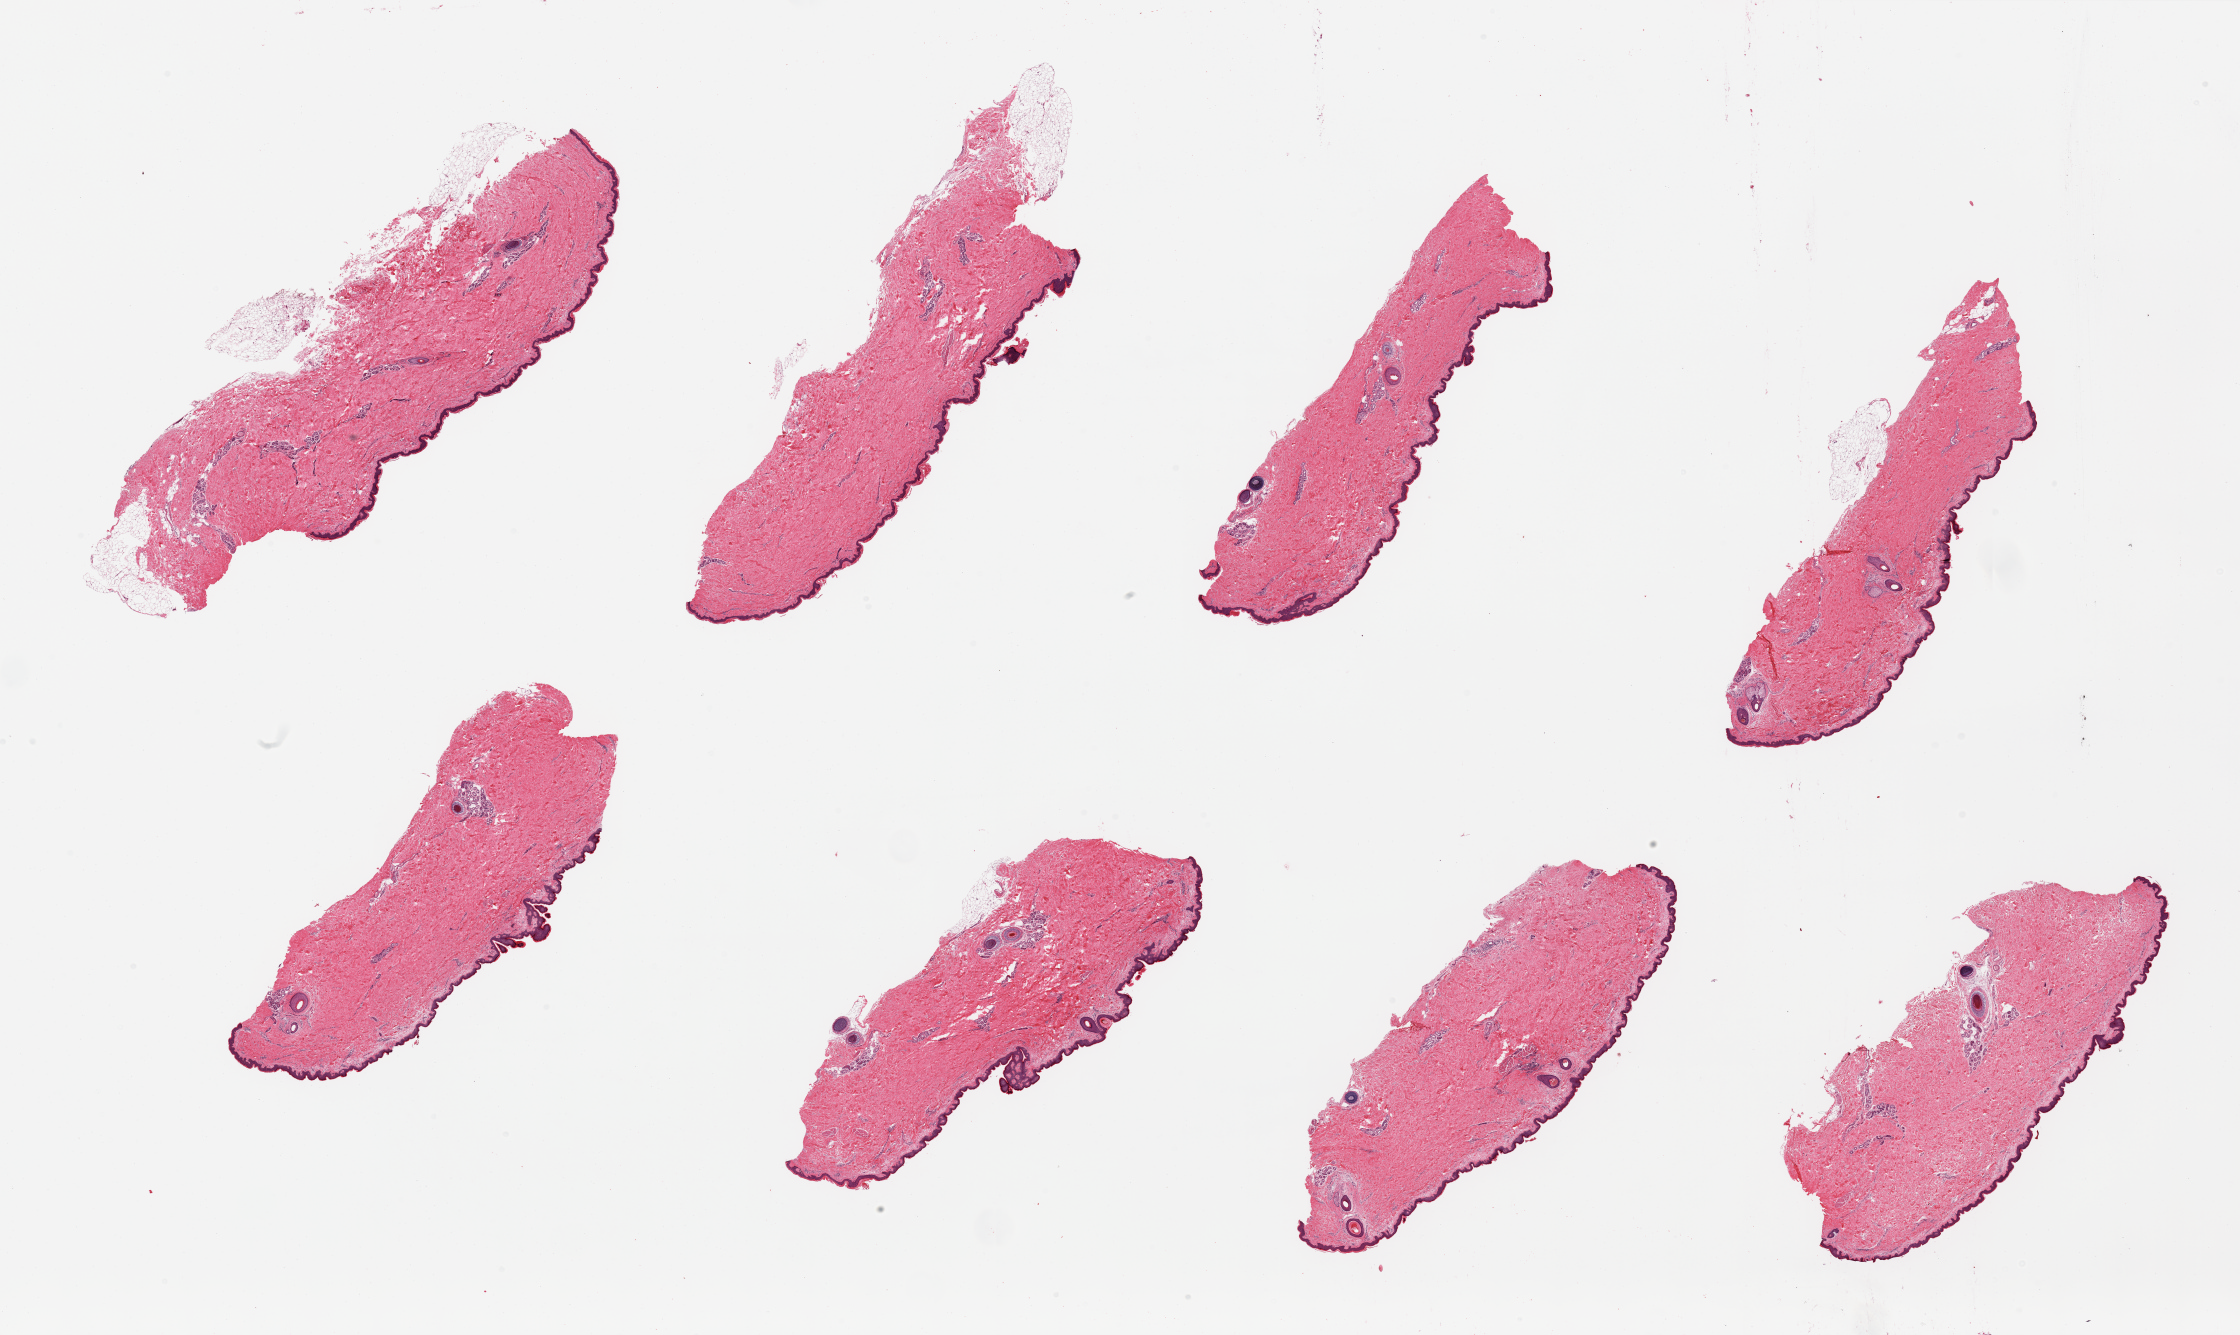
Digitized hematoxylin and eosin (H&E)-stained section — shown as a low-resolution overview of the whole scanned area (about 35.4 x 21.1 mm), PAXgene-fixed paraffin-embedded (PFPE) section, target tissue: skin of suprapubic region, tissue donor sample. Donor sex: male.
Reviewer comment on this tissue sample: 8 pieces, focal adherent dermal fat; squamous epithelium is ~70-80 microns.